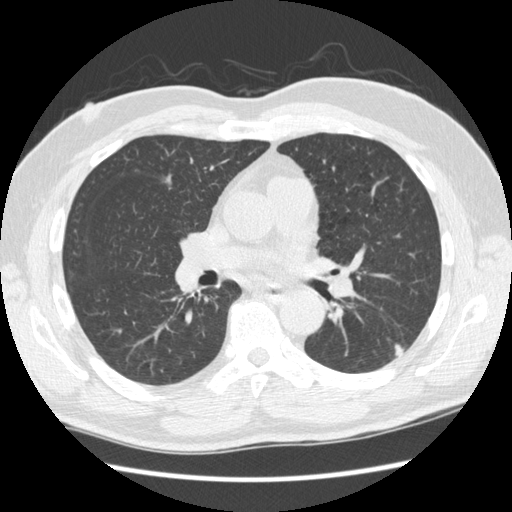
Low-dose screening chest CT, axial slice; baseline annual screen; lung window (W 1500 / L -600 HU). Male participant, aged 74 years at enrolment. Former smoker at enrolment.
• Lesion marked by an expert reader, bounding box (x1, y1, x2, y2) in pixels: (371, 324, 413, 366).
• The screening reader recorded 3 non-calcified nodules or masses ≥4 mm on this exam (right upper lobe, right lower lobe, left upper lobe); which of them this box marks is not recorded.
• Official screen result: positive, change unspecified: nodule(s) >= 4 mm or enlarging nodule(s), mass(es), or other non-specific abnormalities suspicious for lung cancer.
• Lung cancer was diagnosed 384 days after this screen: squamous cell carcinoma, NOS, left lower lobe, well differentiated (G1), stage IA (AJCC 6th edition), 28 mm at pathology.